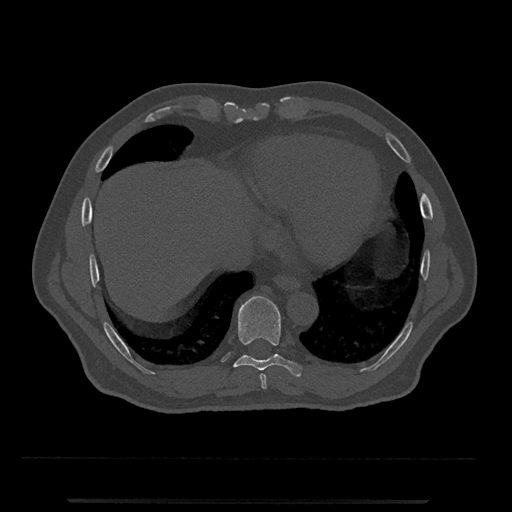
CT including the spine, one axial slice; position 571 of 797 along the scan axis; reconstruction kernel Br40s/3; 120 kVp; bone window (W 1800 / L 400 HU); 0.5 mm slice thickness; 512 × 512 image matrix, field of view 419 × 419 mm. Male patient, age 63 years. Case-level facts recorded for this patient, not image findings: primary cancer: prostate.
Outlined on this slice (semi-automatically segmented with operator editing):
- T8 vertebra: bounding box (x1, y1, x2, y2) in pixels: (260, 374, 267, 390)
- T9 vertebra: (233, 296, 303, 377)